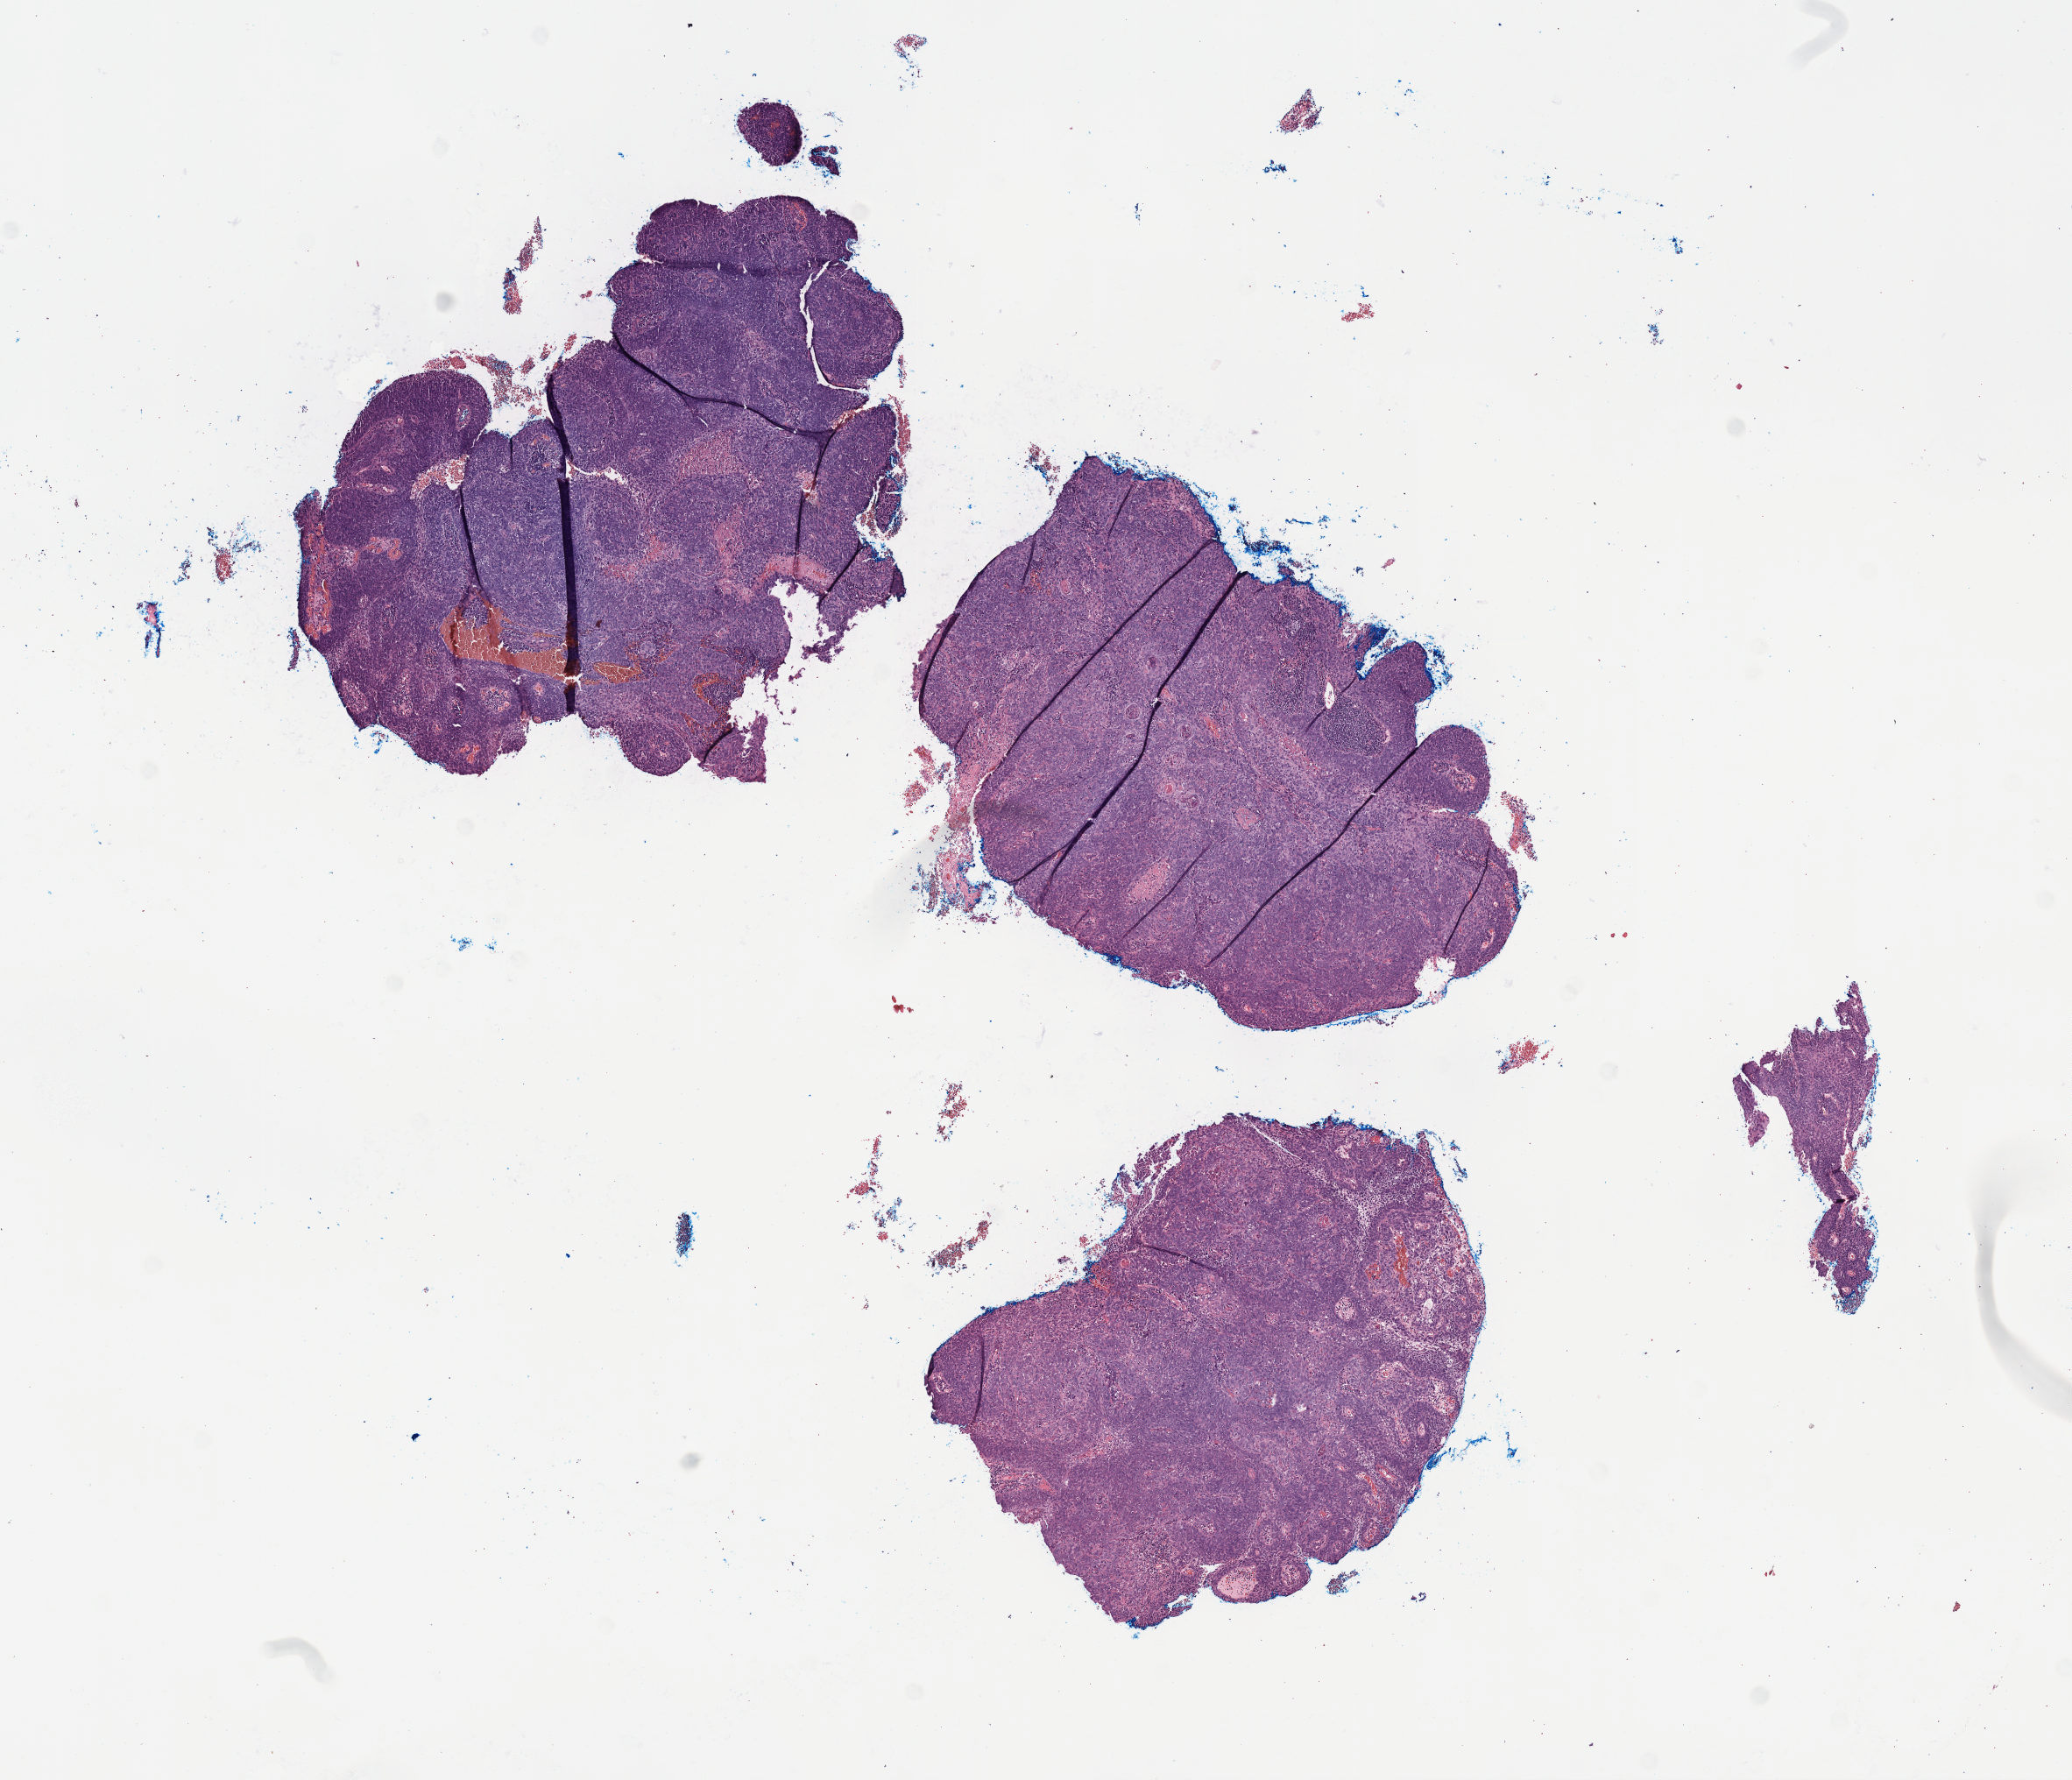
Digitized H&E tissue section (whole slide) — a low-resolution overview of the entire scanned area, about 9.6 x 8.2 mm (from a 40x scan). FFPE section. Sample: primary tumour, cervix. Patient: female, age at initial diagnosis 60 years. Histologic grade: G3 (poorly differentiated).
• FIGO stage: IIIA
• diagnosis: Squamous cell carcinoma, NOS (cervix uteri)